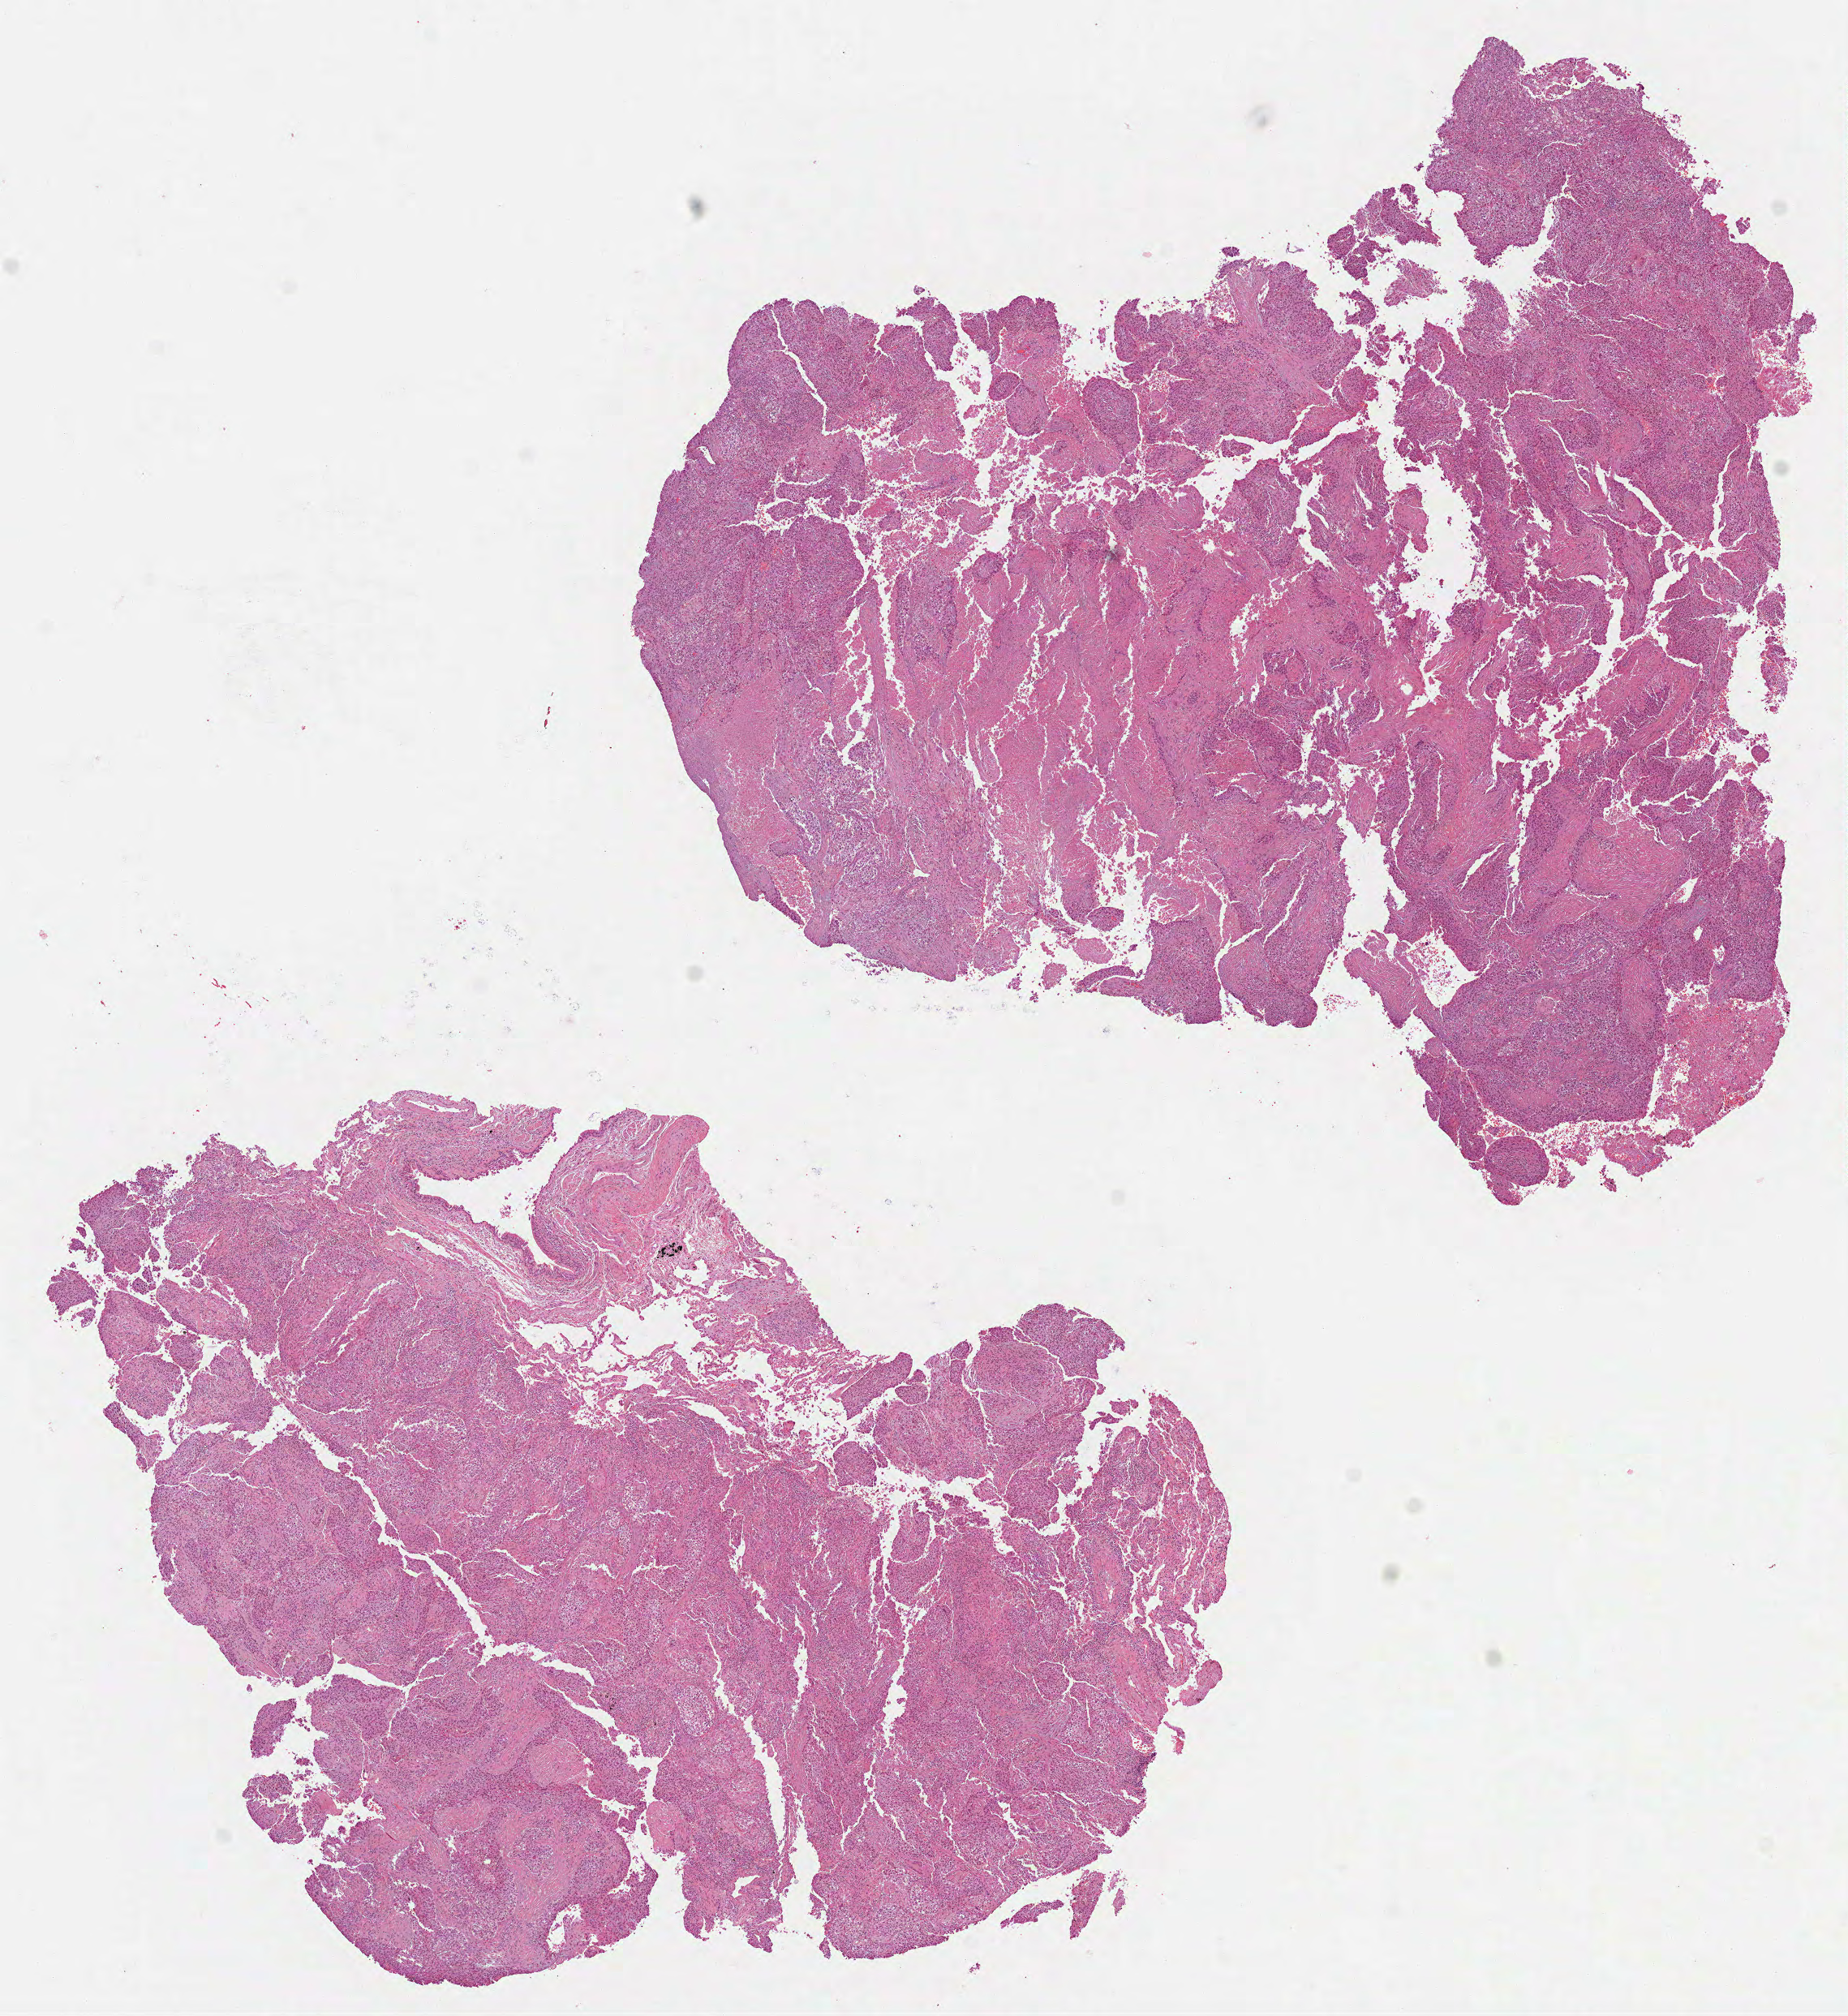
Digitized Hematoxylin and eosin (H&E) stained tissue section (whole slide) — low-resolution overview of the scanned area, about 9.2 x 10.0 mm (acquisition: 40x scan), FFPE section, lung, primary tumour sample. Female, age 76 years at initial diagnosis.
• pathologic diagnosis: Squamous cell carcinoma, NOS (lower lobe, lung)
• AJCC pathologic stage: IB (7th edition)